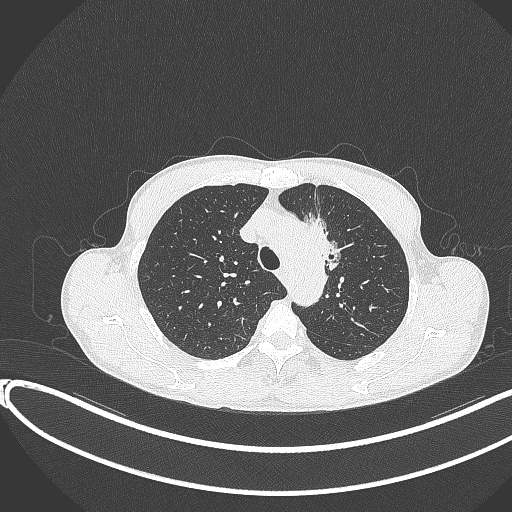
Chest CT, one axial slice. Reconstruction kernel B70f. Lung window (W 1500 / L -600 HU). 1 mm slice thickness. 512 × 512 image matrix, field of view 400 × 400 mm. Male patient, age 58 years. From the clinical record (not read from this slice): clinical TNM (as recorded): T1c N1 M0.
Outlined on this slice (rectangle marked by the reading radiologist):
- lung tumour (recorded histology: adenocarcinoma): bounding box [x1, y1, x2, y2] px = [303, 214, 348, 272]